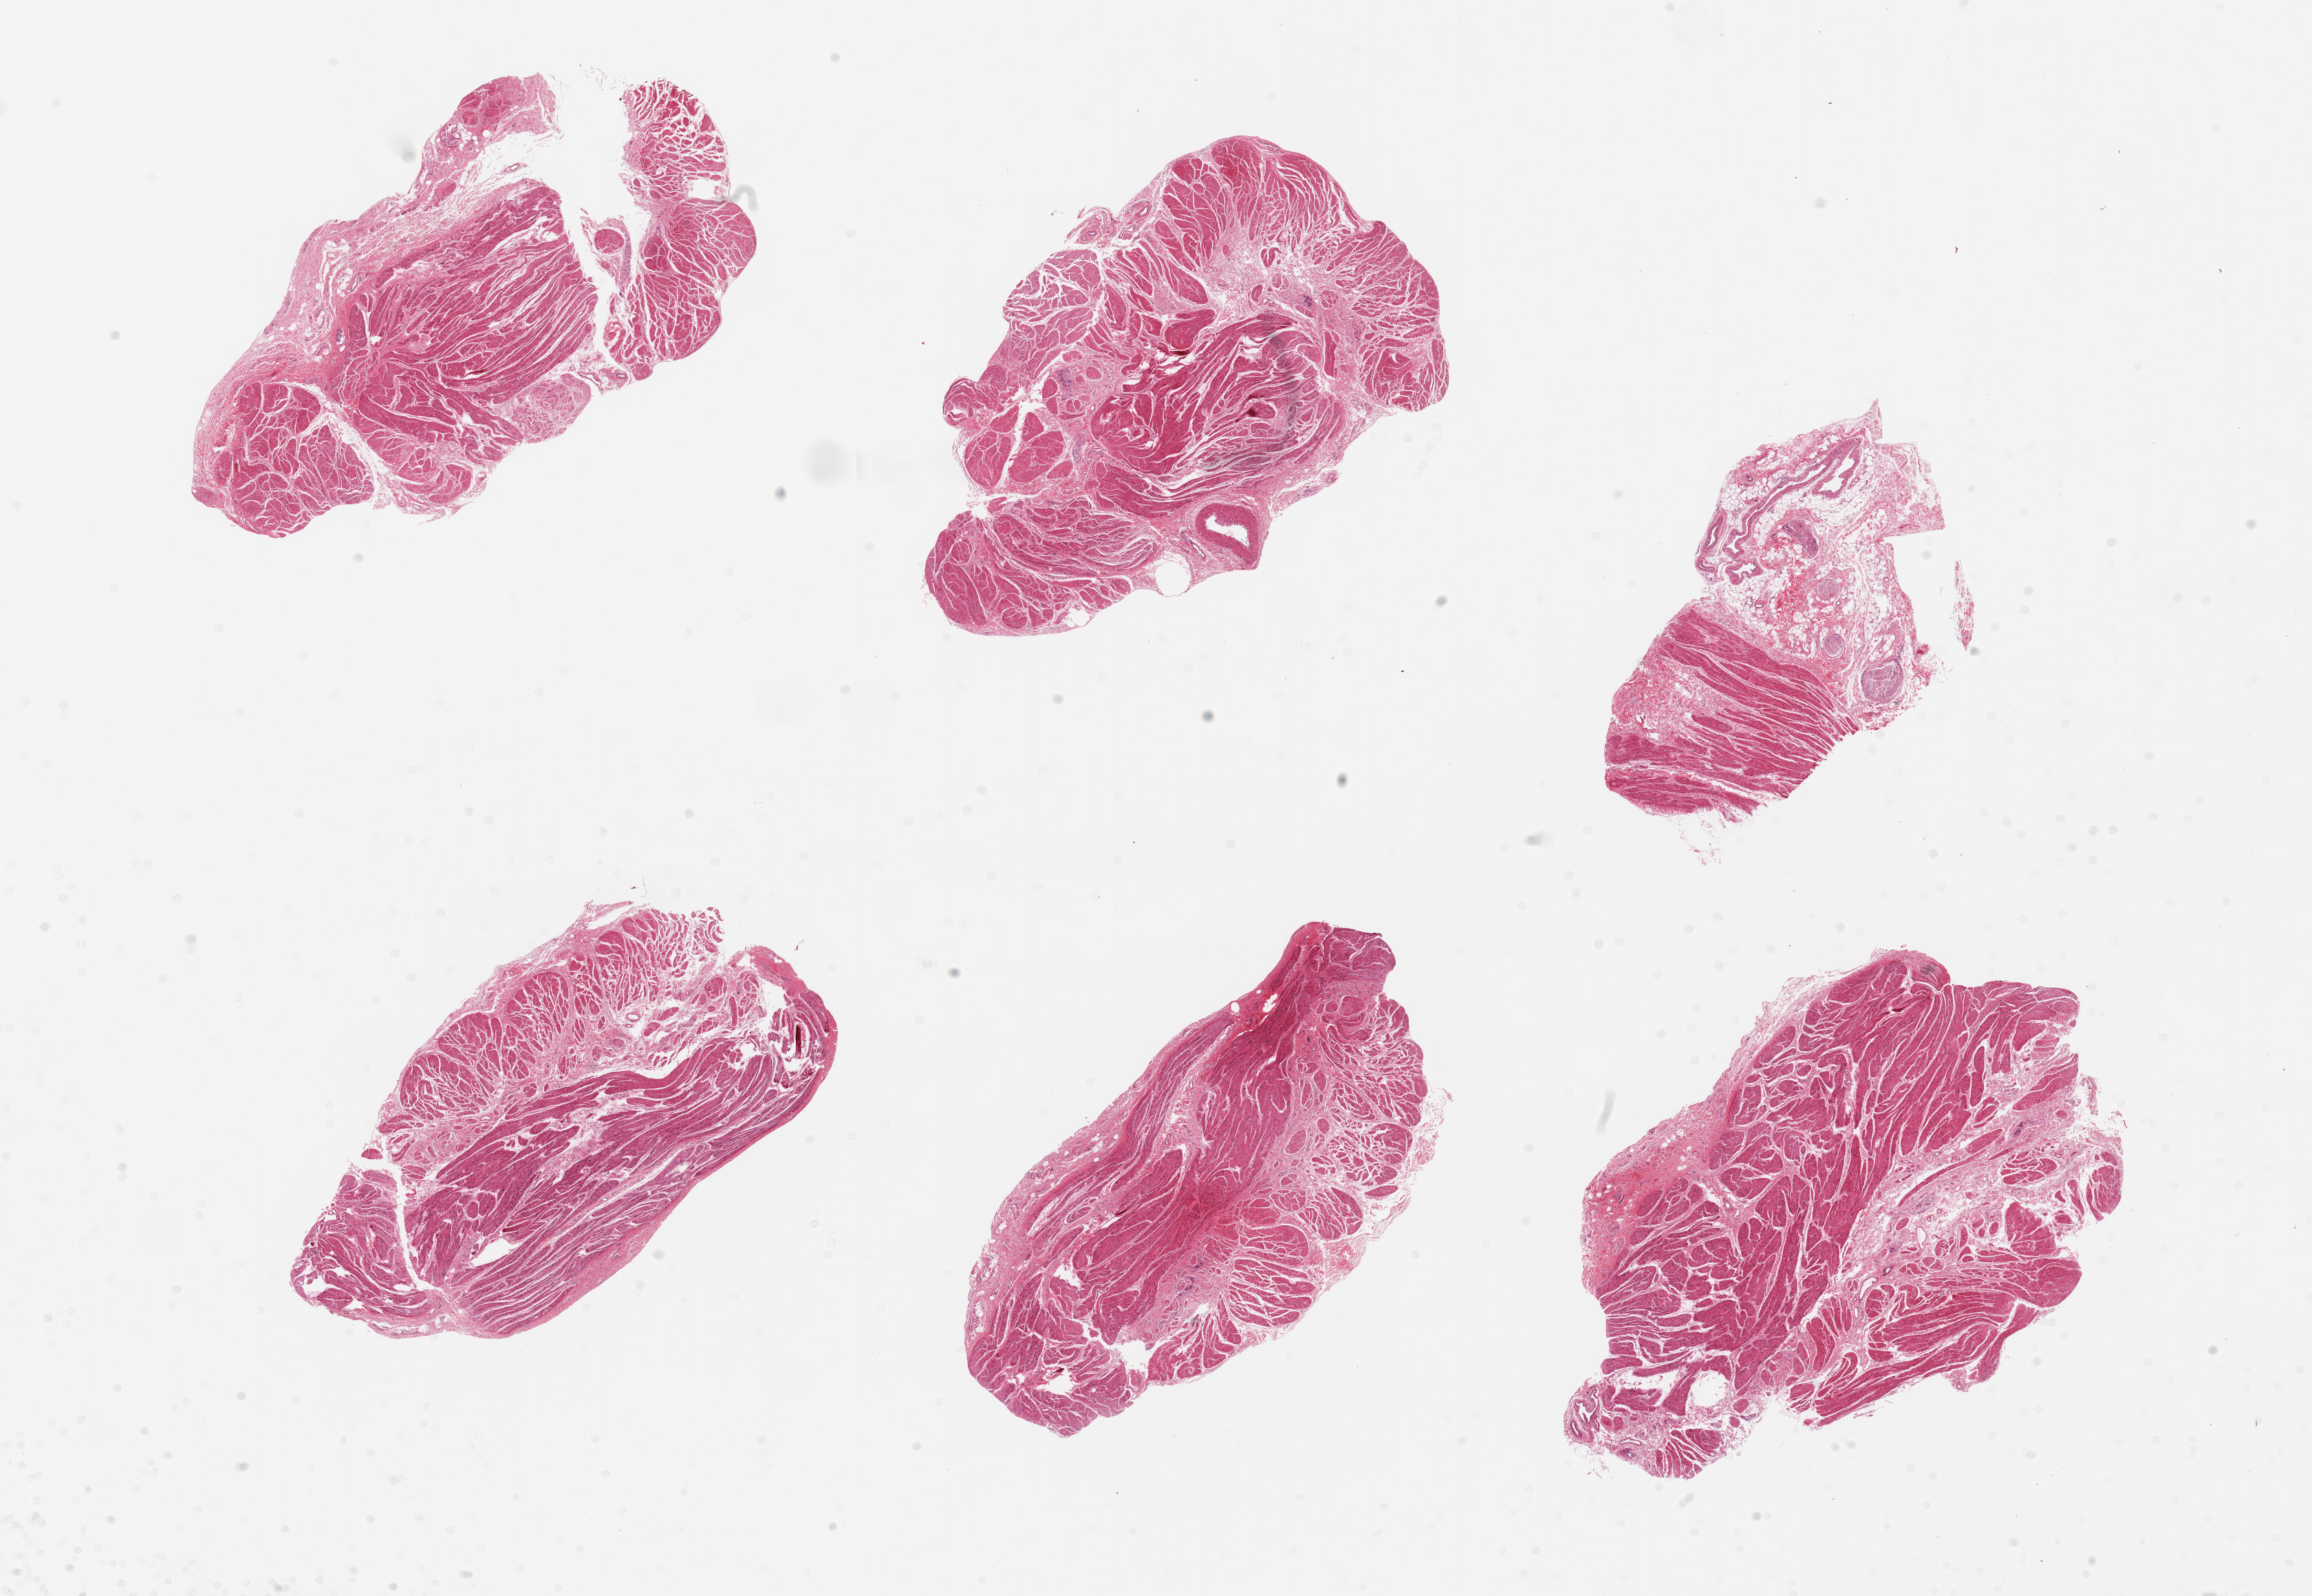
H&E whole-slide image, whole scanned area (about 26.6 x 18.3 mm) shown as a low-resolution overview. PAXgene-fixed, paraffin-embedded tissue. Section of gastroesophageal junction (target tissue). Donor tissue sample. Donor: male.
• review note (as recorded): 6 pieces, all muscularis, focal adherent fat/serosa